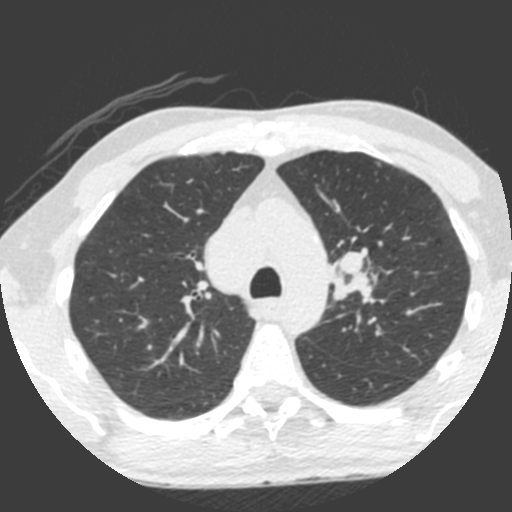
Low-dose screening chest CT, axial slice, third screening round (two years after baseline), lung window (W 1500 / L -600 HU), 2 mm slice thickness. Male, age 55 years at enrolment.
- Lesion marked by an expert reader, bounding box <308,235,387,322> (left, top, right, bottom; pixels).
- Screening reader's record for this exam (one nodule recorded; not confirmed to be the boxed lesion): non-calcified nodule or mass ≥4 mm, left upper lobe, 49 × 29 mm, spiculated (stellate) margins, soft tissue attenuation, pre-existing on the prior screen: yes; interval growth: yes.
- Lung cancer was diagnosed 0 days after this screen: small cell carcinoma, NOS, left upper lobe, undifferentiated (G4), stage IV (AJCC 6th edition), 60 mm at pathology.